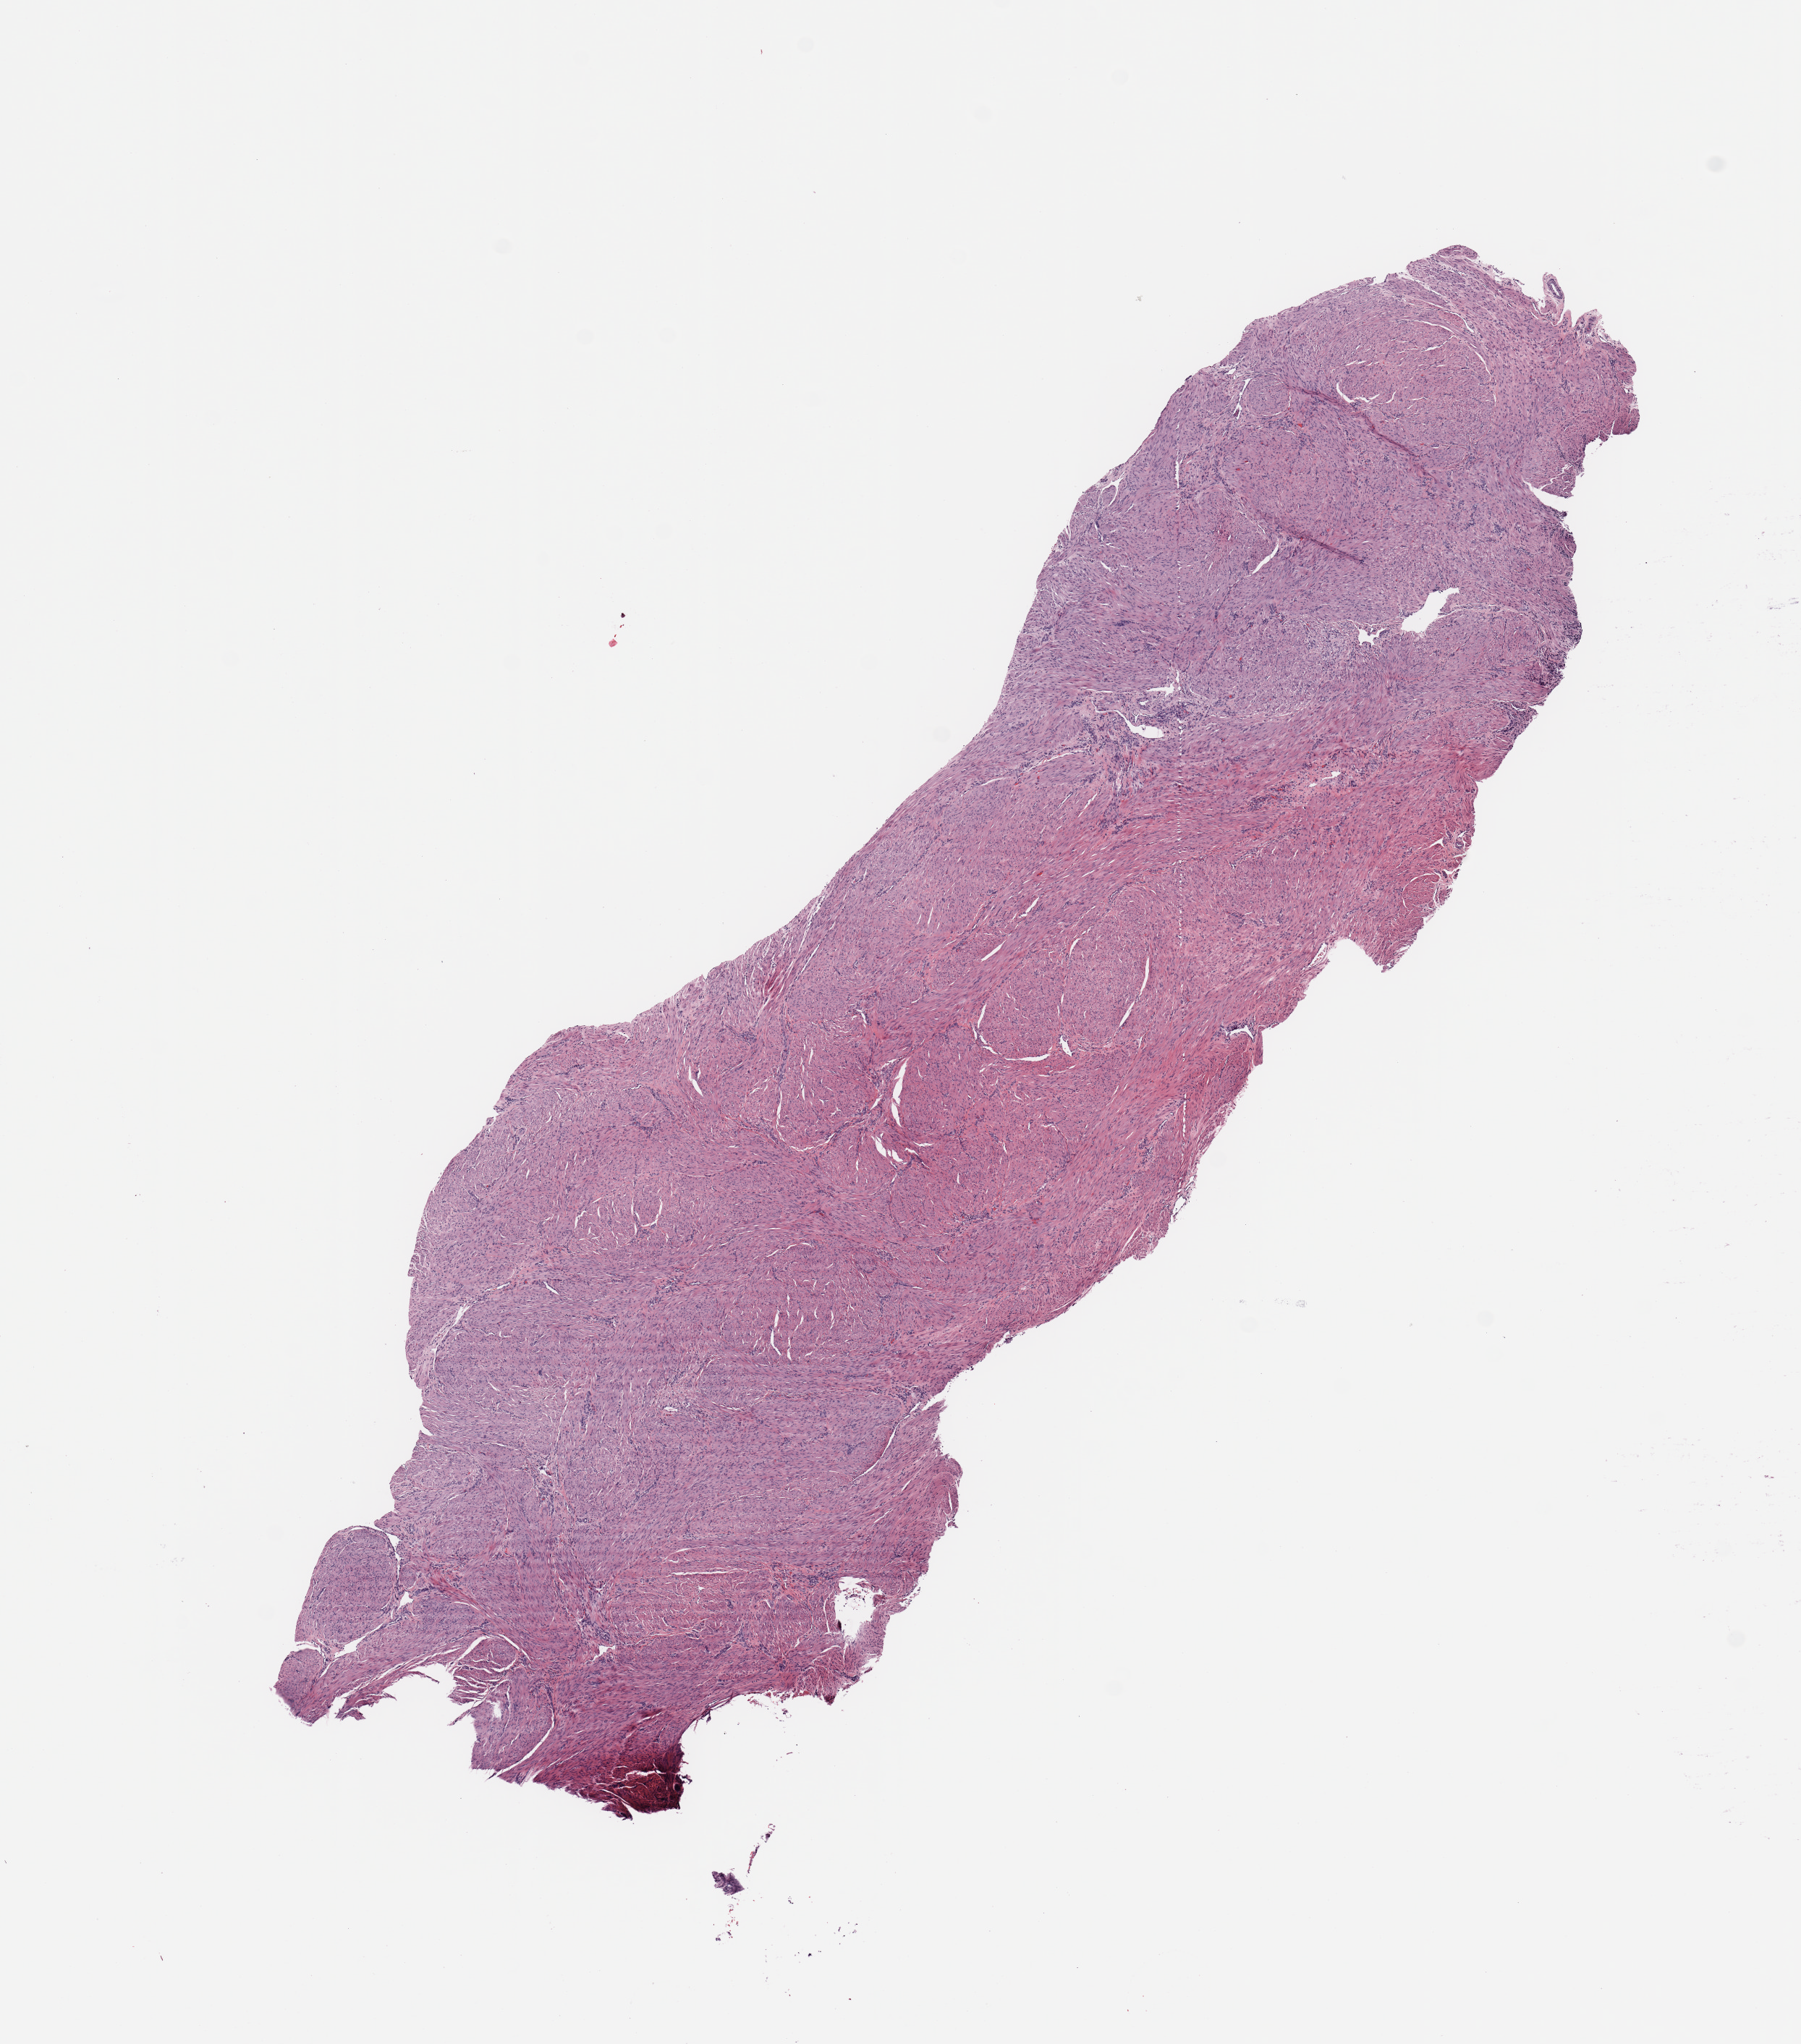
Digitized H&E tissue section (whole slide) — a low-resolution overview of the entire scanned area, about 9.8 x 11.2 mm (slide scanned at 20x), uterus, normal (non-tumour) tissue. Patient: female, age 42 years.
This section: normal (non-tumour) tissue from the same patient. Patient diagnosis: Endometrioid adenocarcinoma, NOS.